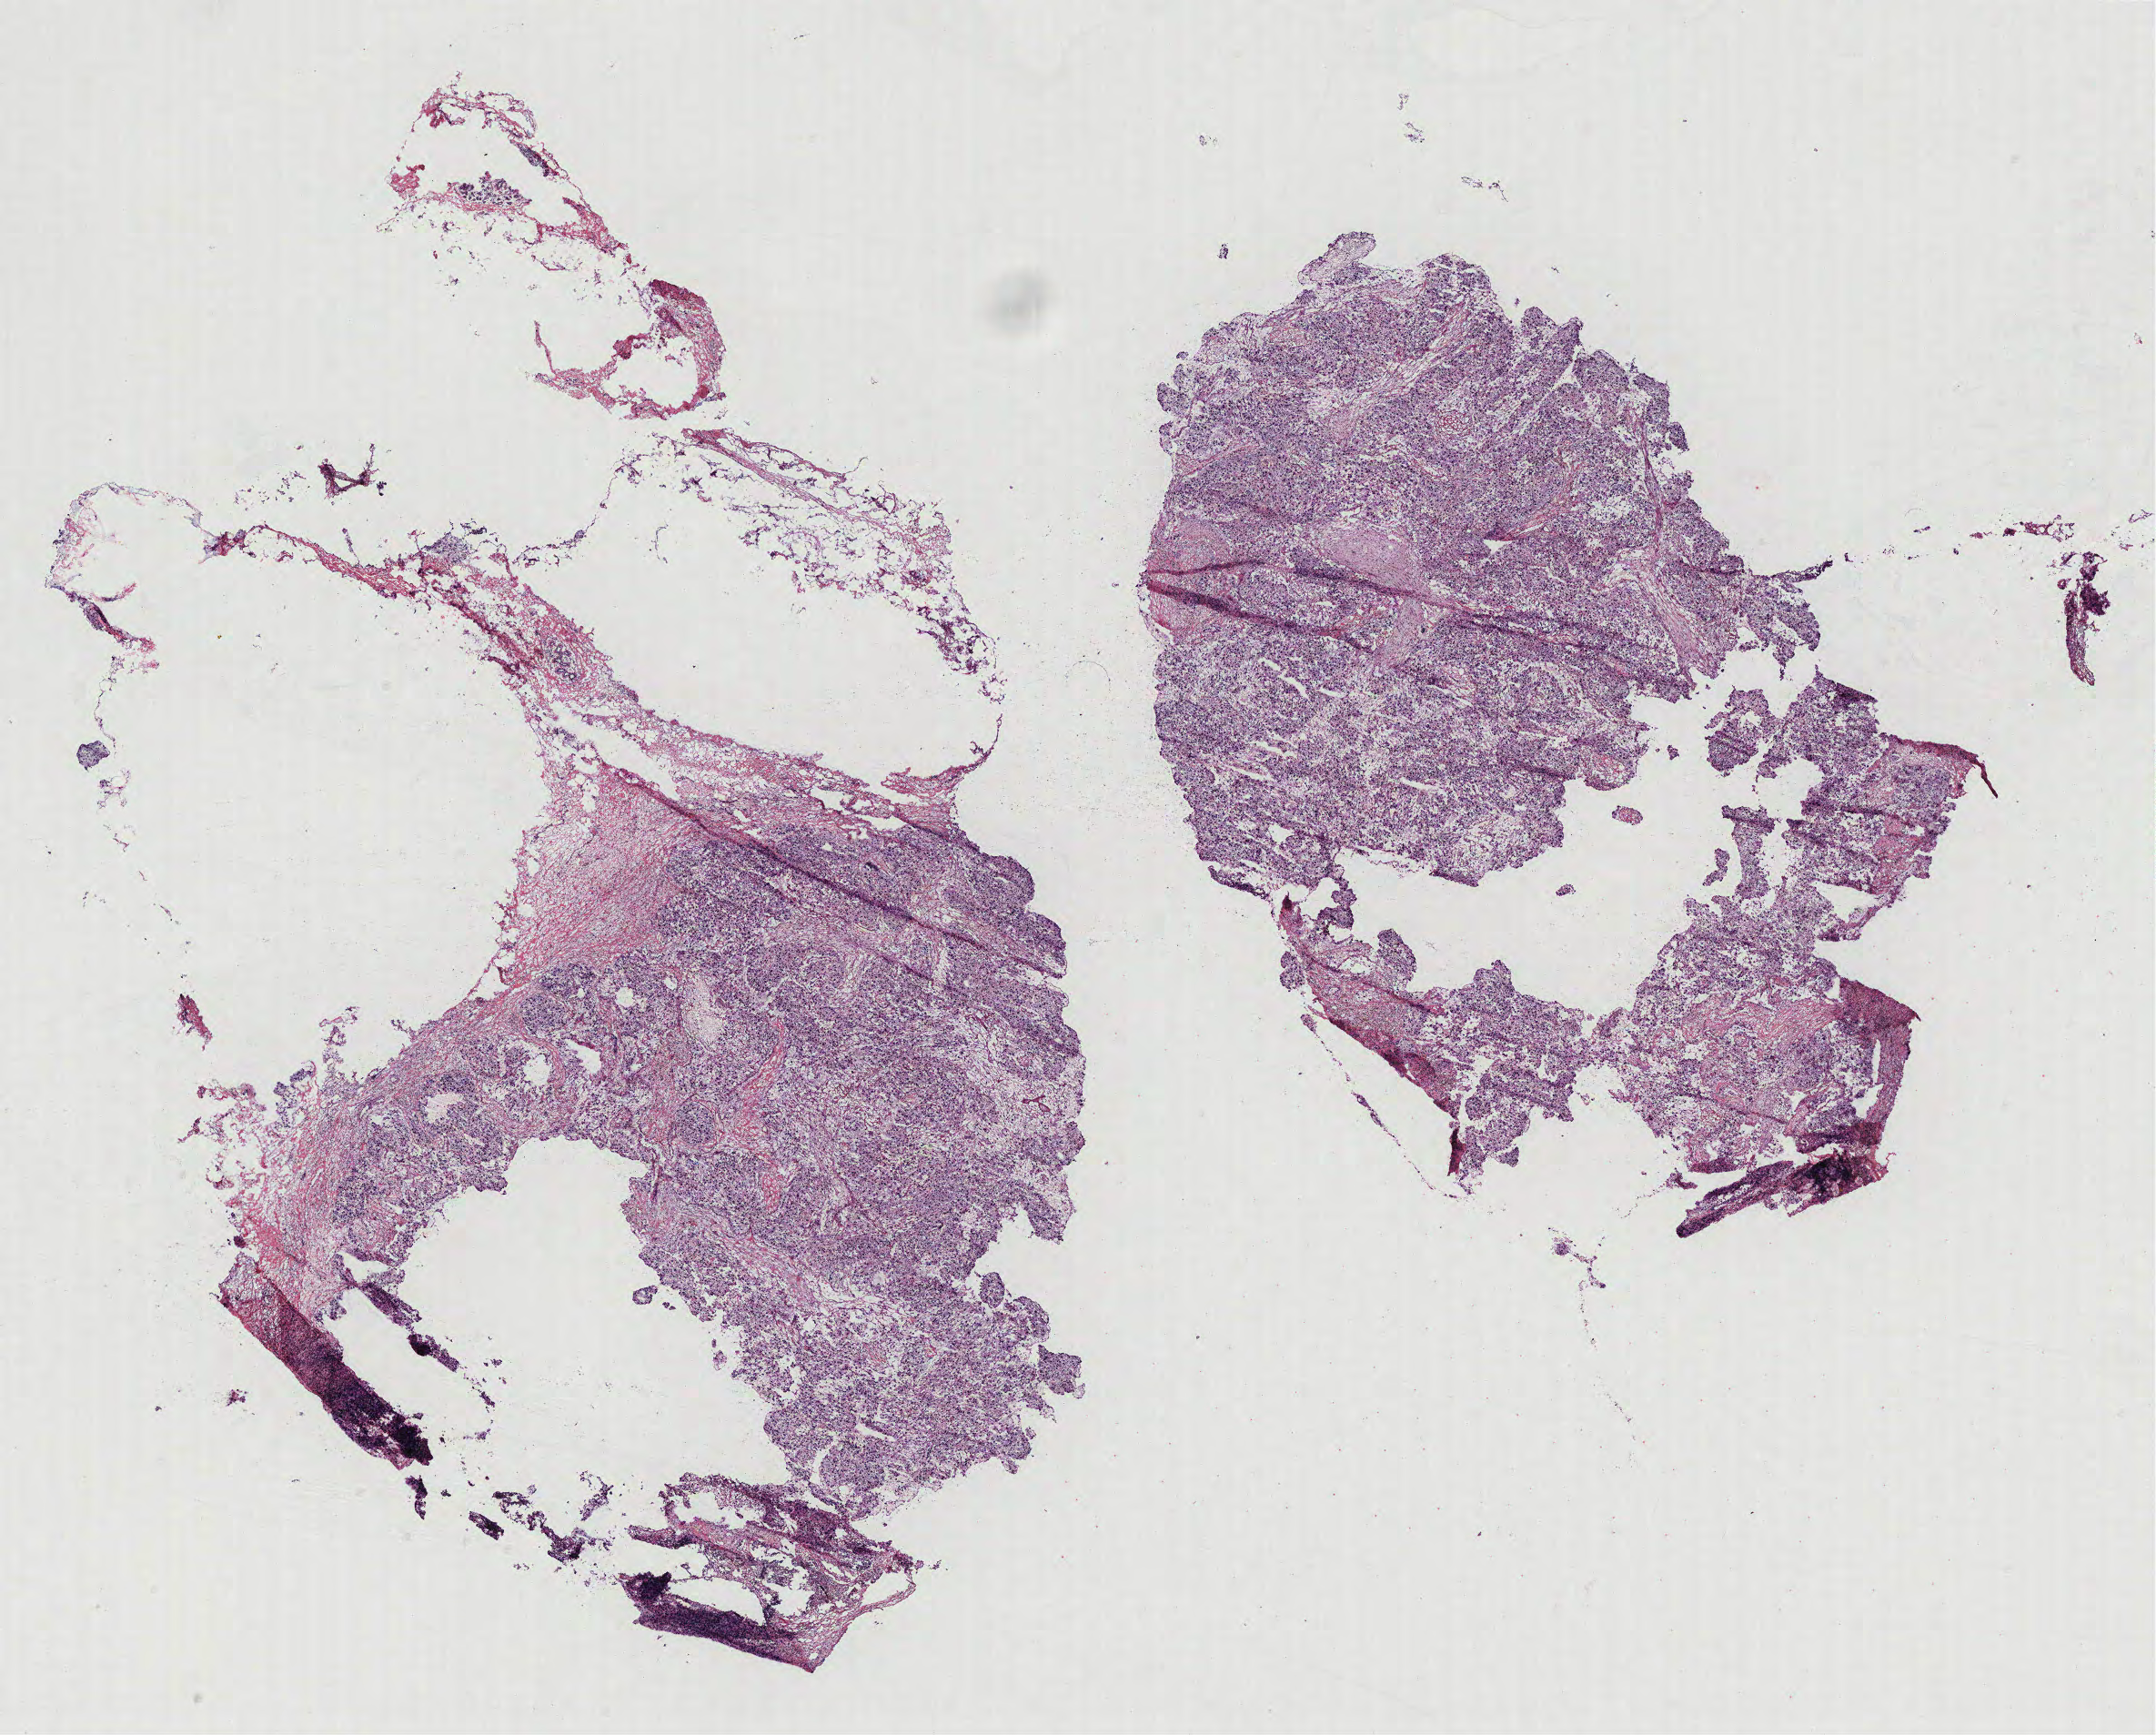
Digitized Hematoxylin and eosin (H&E) stained tissue section (whole slide) — a low-resolution overview of the entire scanned area, about 19.0 x 15.3 mm (slide scanned at 40x), breast, tissue type not recorded.
- patient diagnosis (cohort enrolment): breast cancer (breast)